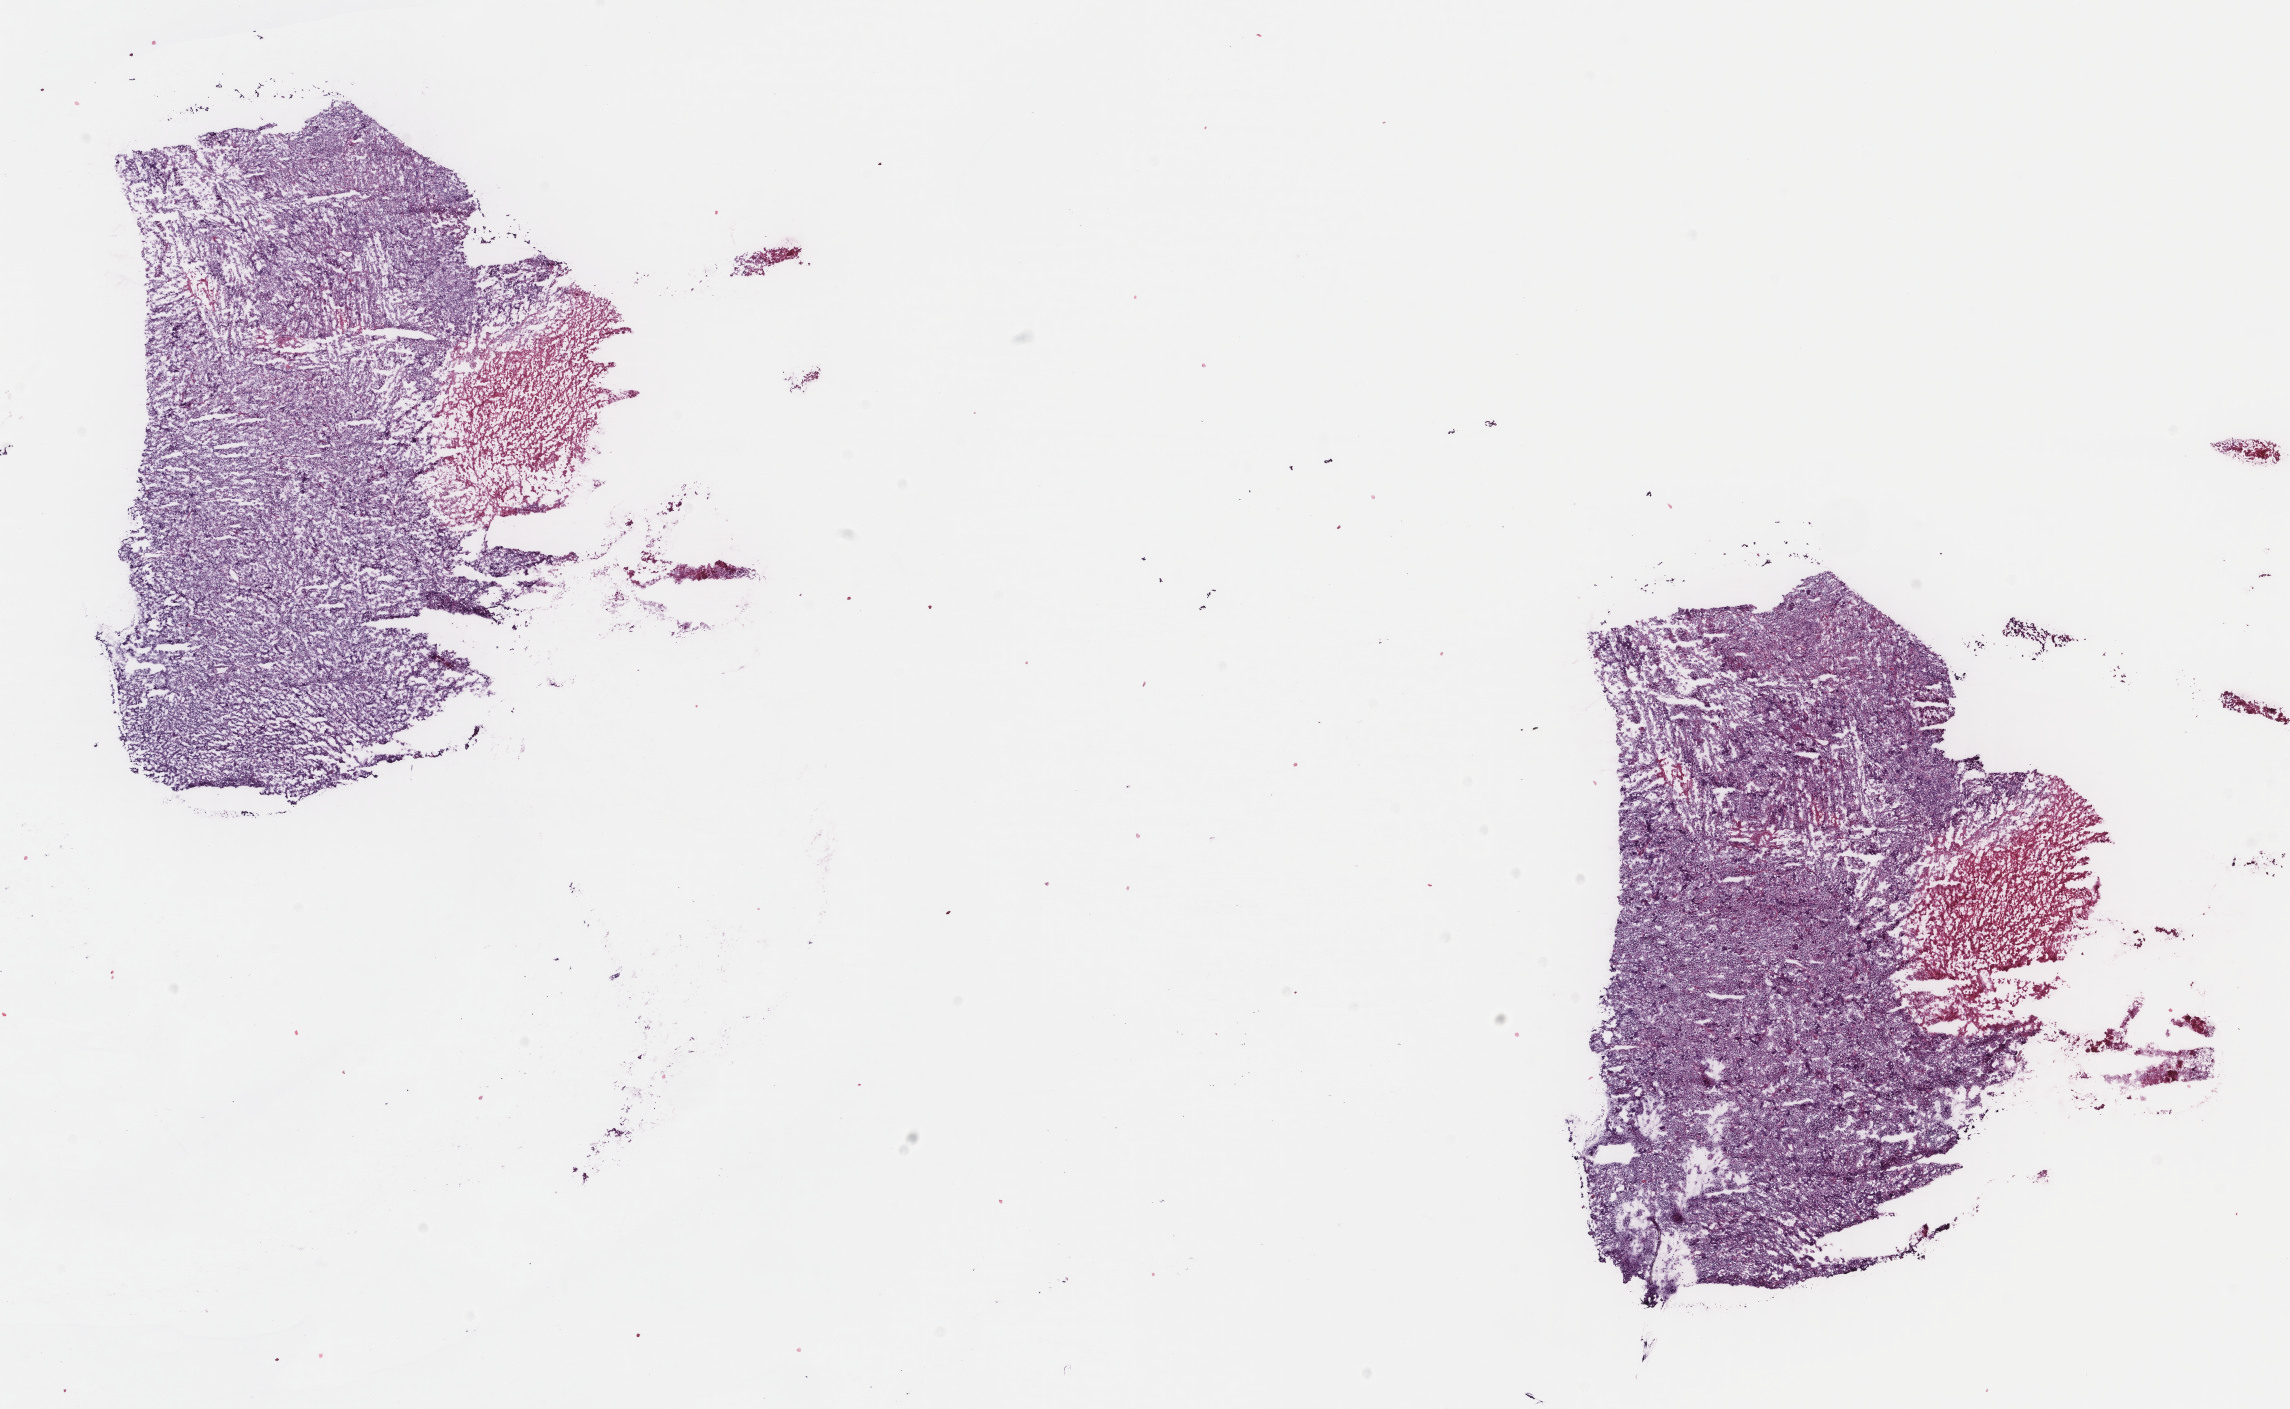
Digitized H&E tissue section (whole slide) — shown as a low-resolution overview of the whole scanned area (about 18.2 x 11.2 mm, slide scanned at 40x), frozen section from the top of the tissue portion, sample: primary tumour, uterus. Female patient; age at initial diagnosis 82 years. Histologic grade: G3 (poorly differentiated). Slide review estimates, as recorded: tumour cells 88%, tumour nuclei 98%, normal cells 0%, stromal cells 2%, necrosis 10%. Infiltration values recorded for this section: lymphocyte infiltration 40%, monocyte infiltration 35%, neutrophil infiltration 2%.
Pathologic diagnosis: Endometrioid adenocarcinoma, NOS. FIGO stage: IB.